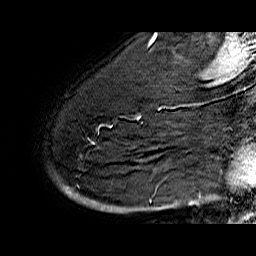
Breast MRI (dynamic contrast-enhanced), one sagittal slice. Slice 47 of 60 in the series (ordered by position). Dynamic contrast-enhanced series, time point 2 of 6 at this slice position (early post-contrast). 1.5 T. TE 6.4 ms, TR 32.9 ms. 4 mm slice thickness. 256 × 256 image matrix, field of view 200 × 200 mm. Female patient. Case-level facts recorded for this patient, not image findings: setting: breast cancer imaged before/during neoadjuvant chemotherapy; receptor status: HR-positive, HER2-negative.
Structures marked on this image (semi-automatically segmented with operator editing):
- analysis volume of interest (the breast-tissue region the enhancement analysis was run in; not a lesion): bounding box <55,74,176,210> (left, top, right, bottom; pixels)
- tumour enhancement mask (voxels above the 100 % enhancement threshold inside the analysis volume of interest): <65,115,141,196>